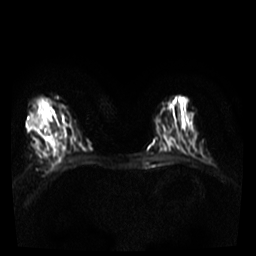
Breast MRI, one axial slice. Diffusion-weighted series; image 2 of 4 stored at this slice position (different b-values; order by instance number). 3 T. 5 mm slice thickness. 256 × 256 image matrix, field of view 300 × 300 mm. Female patient.
Annotated regions visible in this slice (expert manual segmentation):
- tumour on diffusion-weighted imaging: box from (x=34, y=116) to (x=55, y=147) px